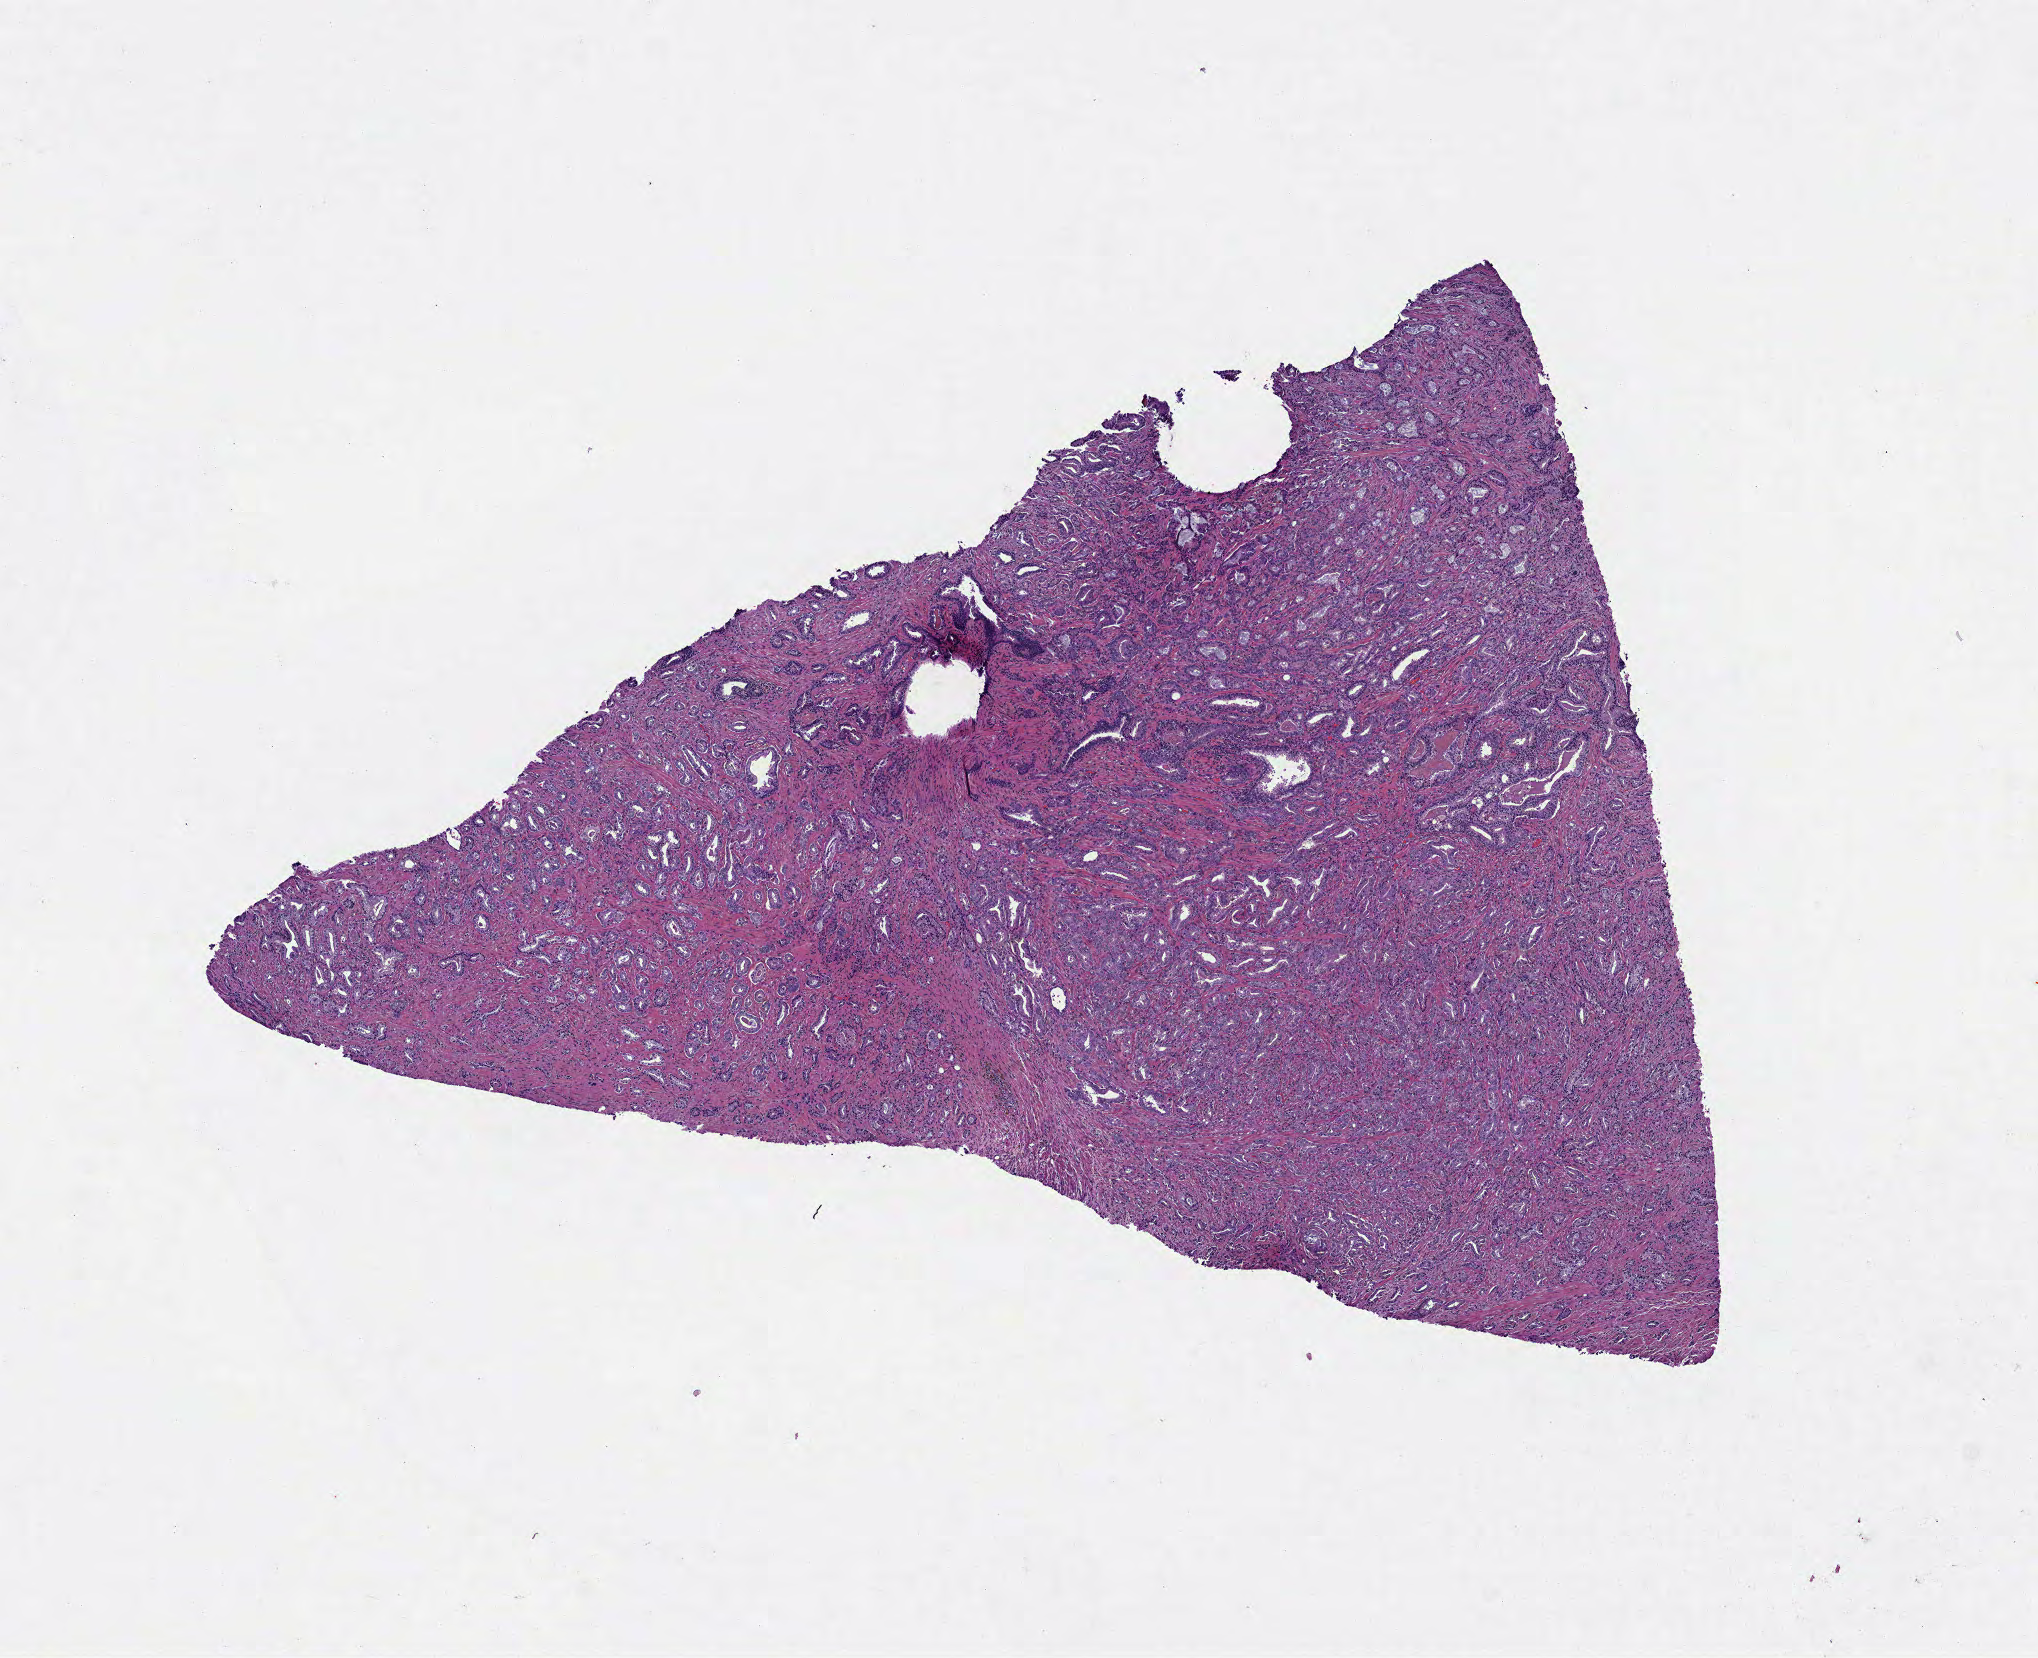
Digitized H&E tissue section (whole slide), shown as a low-resolution overview of the whole scanned area (about 8.2 x 6.7 mm), formalin-fixed paraffin-embedded (FFPE) diagnostic section, sample: primary tumour, prostate. Patient: male, age at initial diagnosis 68 years.
Diagnosis: Adenocarcinoma, NOS.